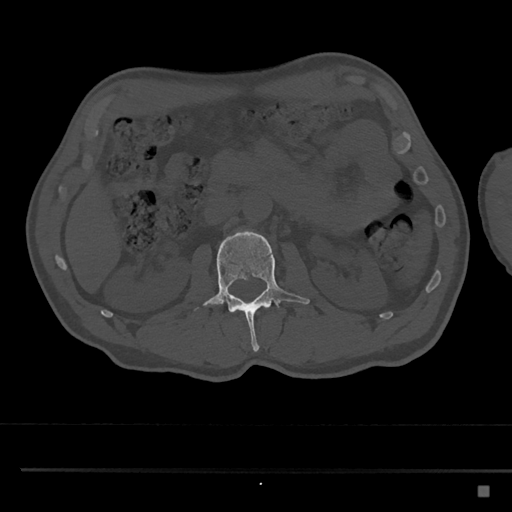
CT including the spine, one axial slice. Position 761 of 797 along the scan axis. Reconstruction kernel Br40s/3. Bone window (W 1800 / L 400 HU). 0.5 mm slice thickness. 512 × 512 image matrix, field of view 391 × 391 mm. Patient: male, 59 years. From the clinical record (not read from this slice): primary cancer: prostate.
Outlined on this slice (semi-automatic segmentation, software-assisted and operator-edited):
- L2 vertebra: bounding box [x1, y1, x2, y2] px = [203, 230, 310, 352]